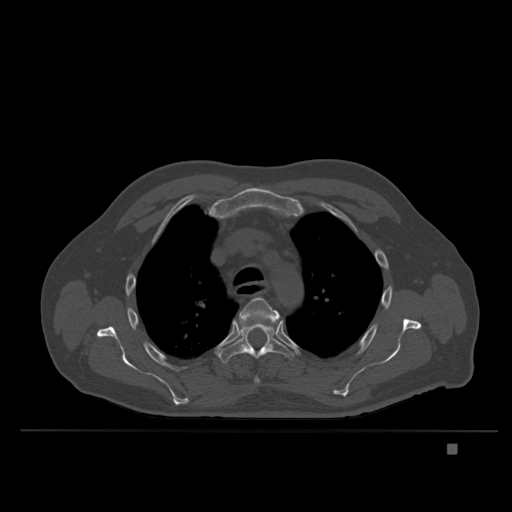
CT including the spine, one axial slice; position 279 of 435 along the scan axis; bone window (W 1800 / L 400 HU); 512 × 512 image matrix. Patient: male, 73 years. Case-level facts recorded for this patient, not image findings: primary cancer: skin.
Structures marked on this image (semi-automatic segmentation, software-assisted and operator-edited):
- T4 vertebra: bounding box [x1, y1, x2, y2] px = [237, 297, 280, 384]
- T5 vertebra: [219, 321, 295, 363]